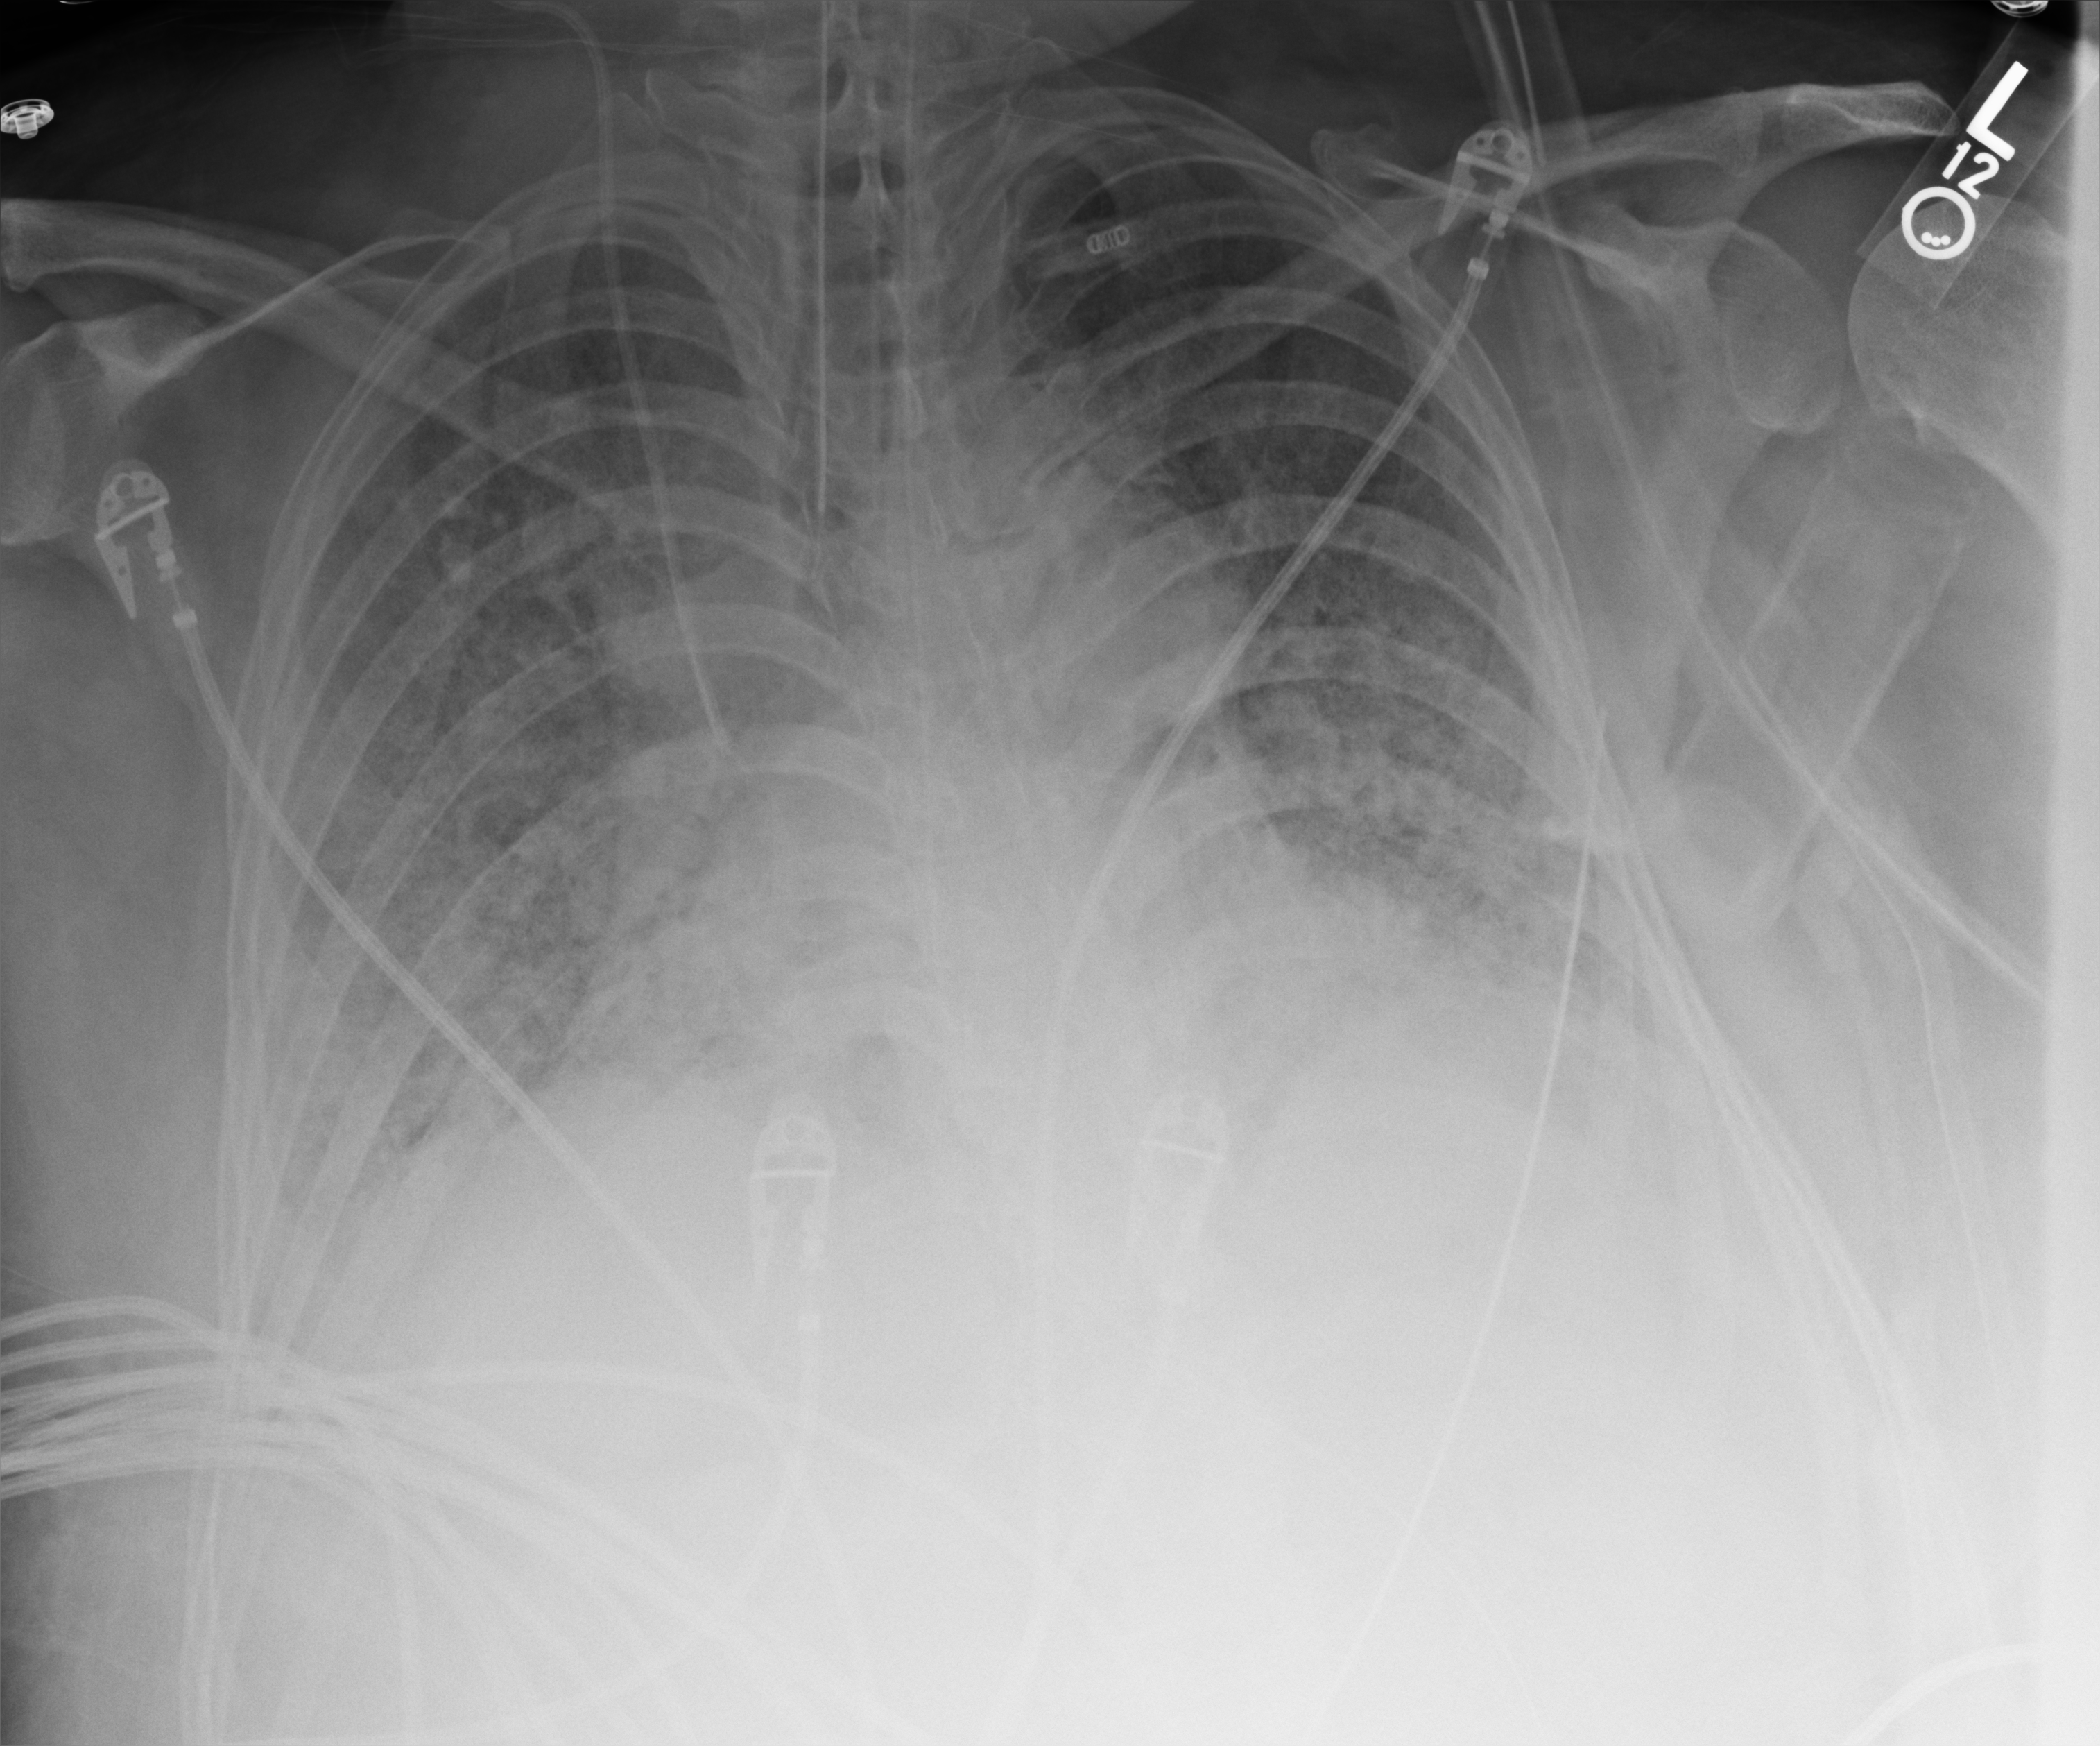
Portable chest radiograph; anteroposterior (AP) projection. Adult patient hospitalised with COVID-19, age 18–59 years.
Hospital-stay facts (about this admission, not read from this image; timing relative to this image not recorded): mechanically ventilated during this hospital stay: yes; admitted to intensive care during this hospital stay: yes.